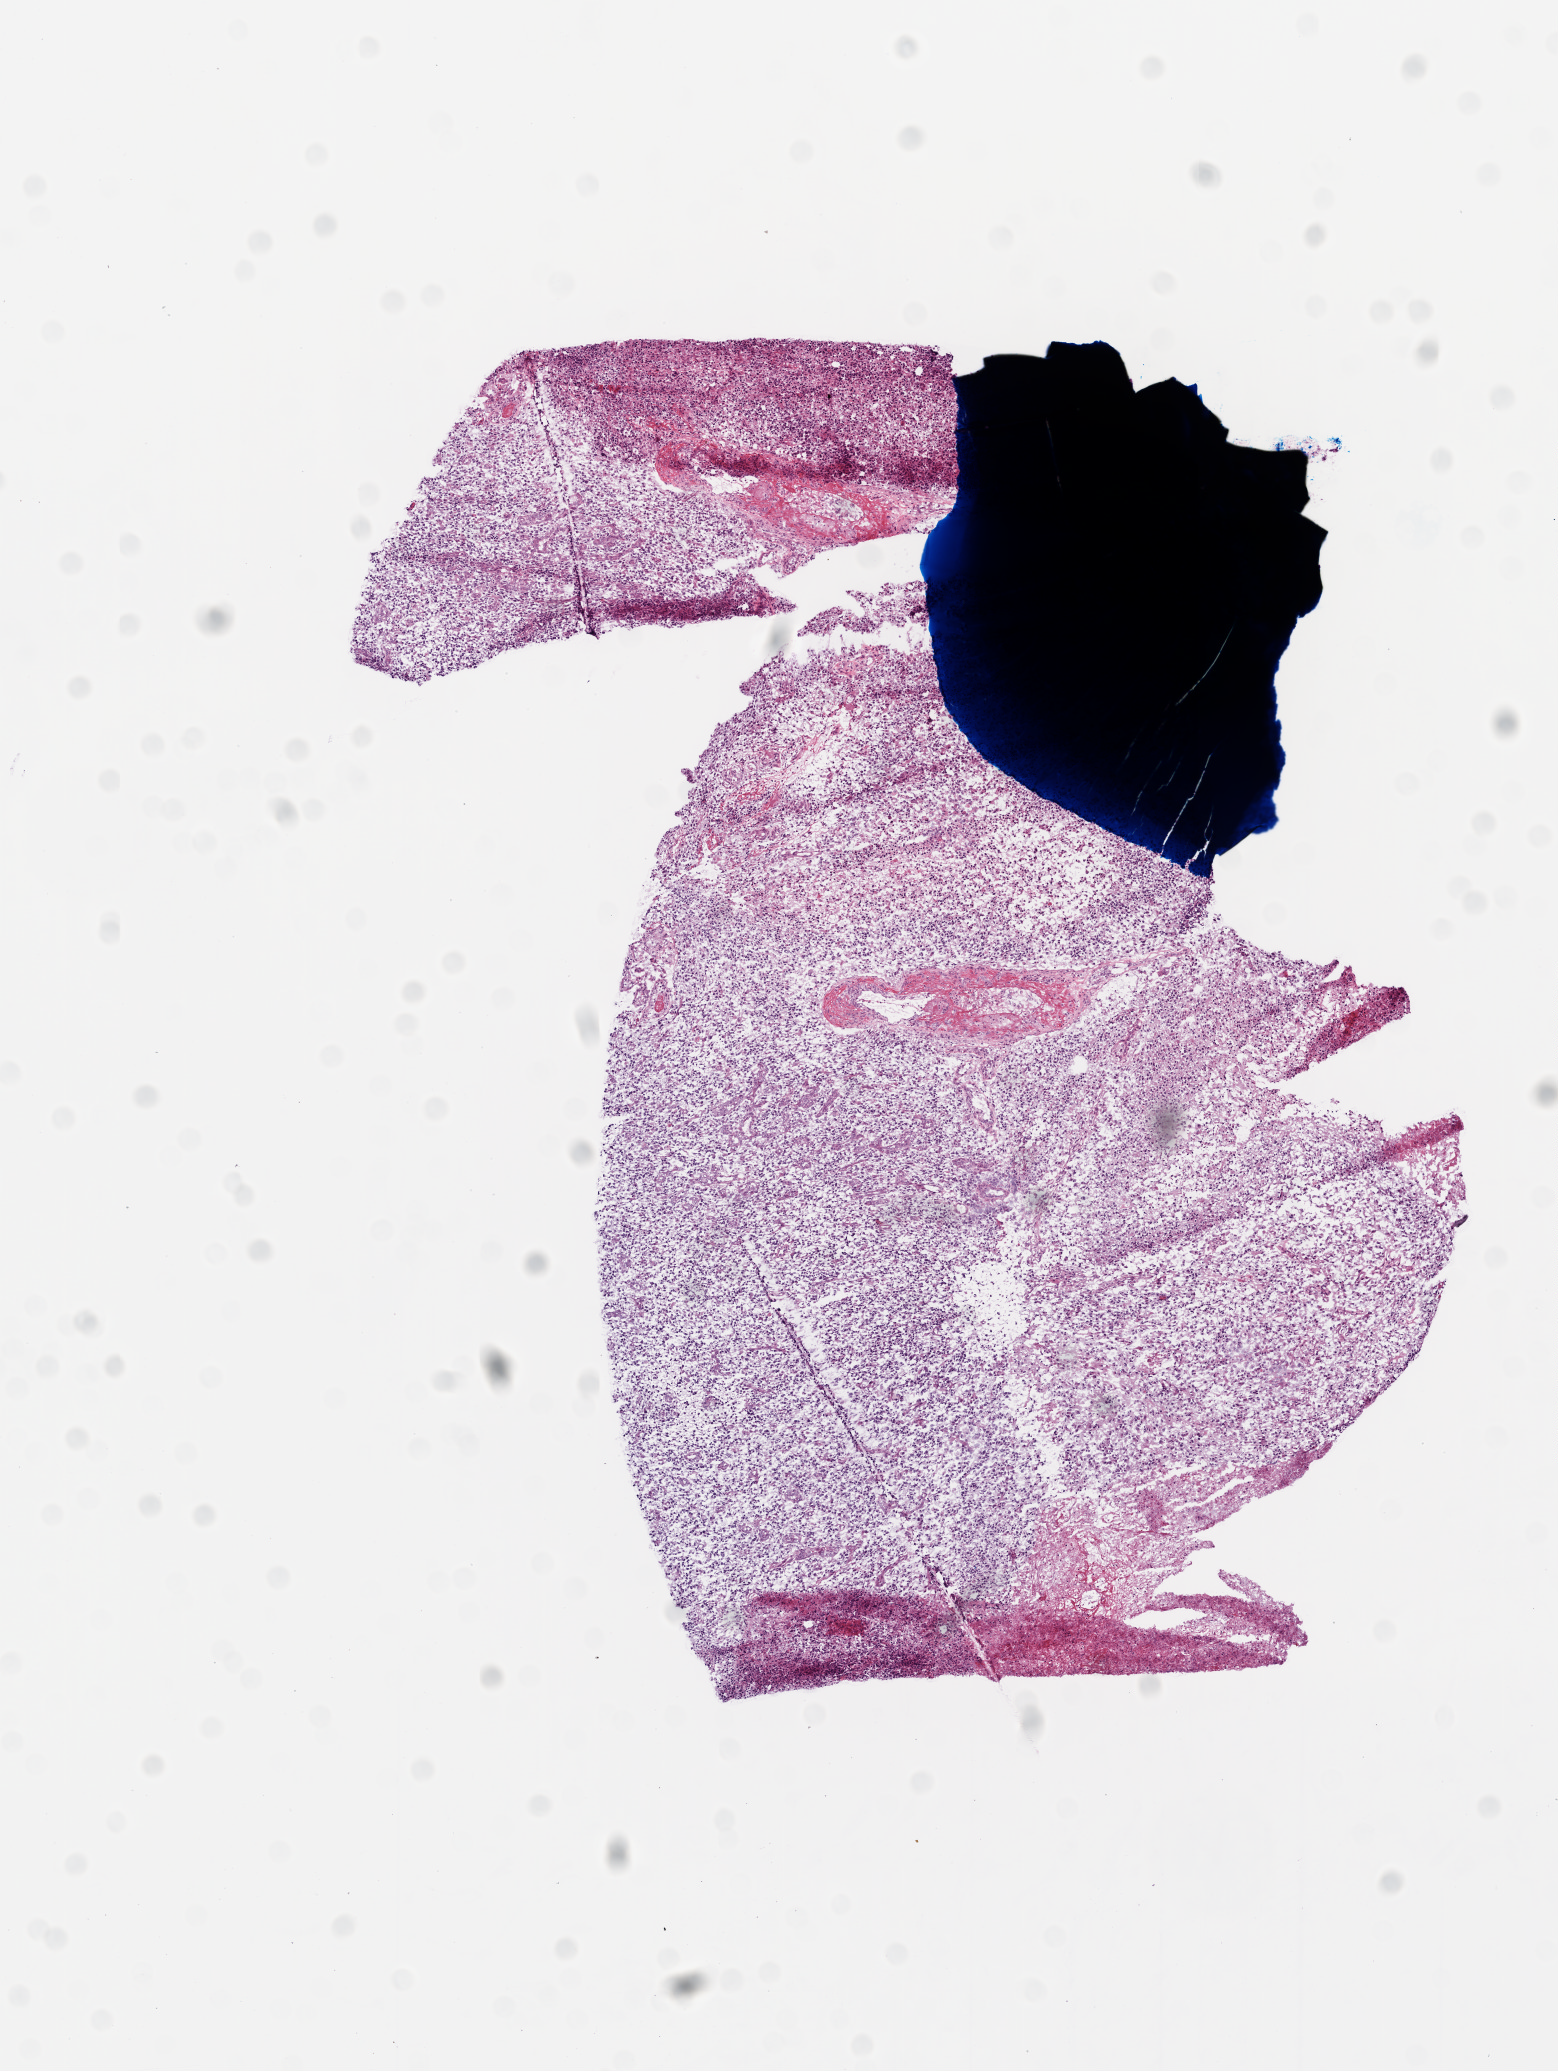
Whole-slide histology image, Hematoxylin and eosin (H&E) stained, a low-resolution overview of the entire scanned area, about 6.3 x 8.4 mm. Frozen section from the top of the tissue portion. Primary tumour sample from the brain. Male, age 59 years at initial diagnosis. Composition of this section per pathologist review: tumour cells 95%, tumour nuclei 100%.
Diagnosis: Glioblastoma.